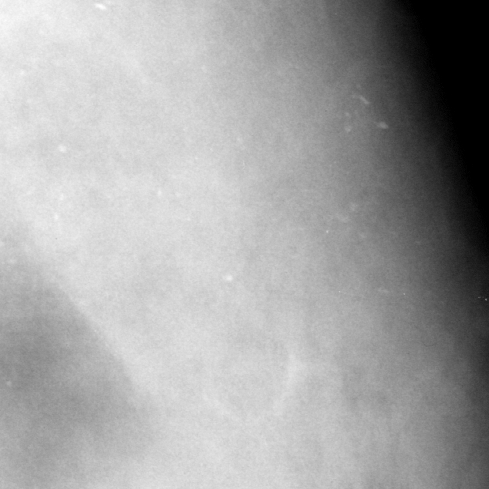
Region of interest cut from a scanned film mammogram (one marked finding); left breast; MLO view; BI-RADS breast density category 4 (scale 1–4).
Marked abnormality: calcifications, morphology round and regular / punctate / amorphous, distribution regional; BI-RADS assessment category 4; pathology (as recorded): benign.